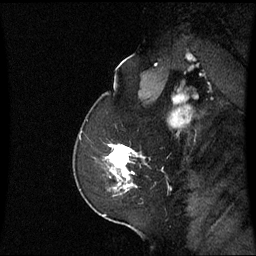
Breast MRI (dynamic contrast-enhanced), one sagittal slice; slice 45 of 60 in the series (ordered by position); dynamic contrast-enhanced series, image 2 of 3 at this slice position (ordered by acquisition); 1.5 T; TE 4.2 ms, TR 8.9 ms; 2.2 mm slice thickness; 256 × 256 image matrix, field of view 220 × 220 mm. Female patient, age 58 years. From the clinical record (not read from this slice): setting: breast cancer imaged before/during neoadjuvant chemotherapy; receptor status: triple-negative.
Outlined on this slice (semi-automatically segmented with operator editing):
- analysis volume of interest (the breast-tissue region the enhancement analysis was run in; not a lesion): box from (x=106, y=144) to (x=143, y=191) px
- tumour enhancement mask (voxels above the 70 % enhancement threshold inside the analysis volume of interest): (x=108, y=144)–(x=135, y=187)